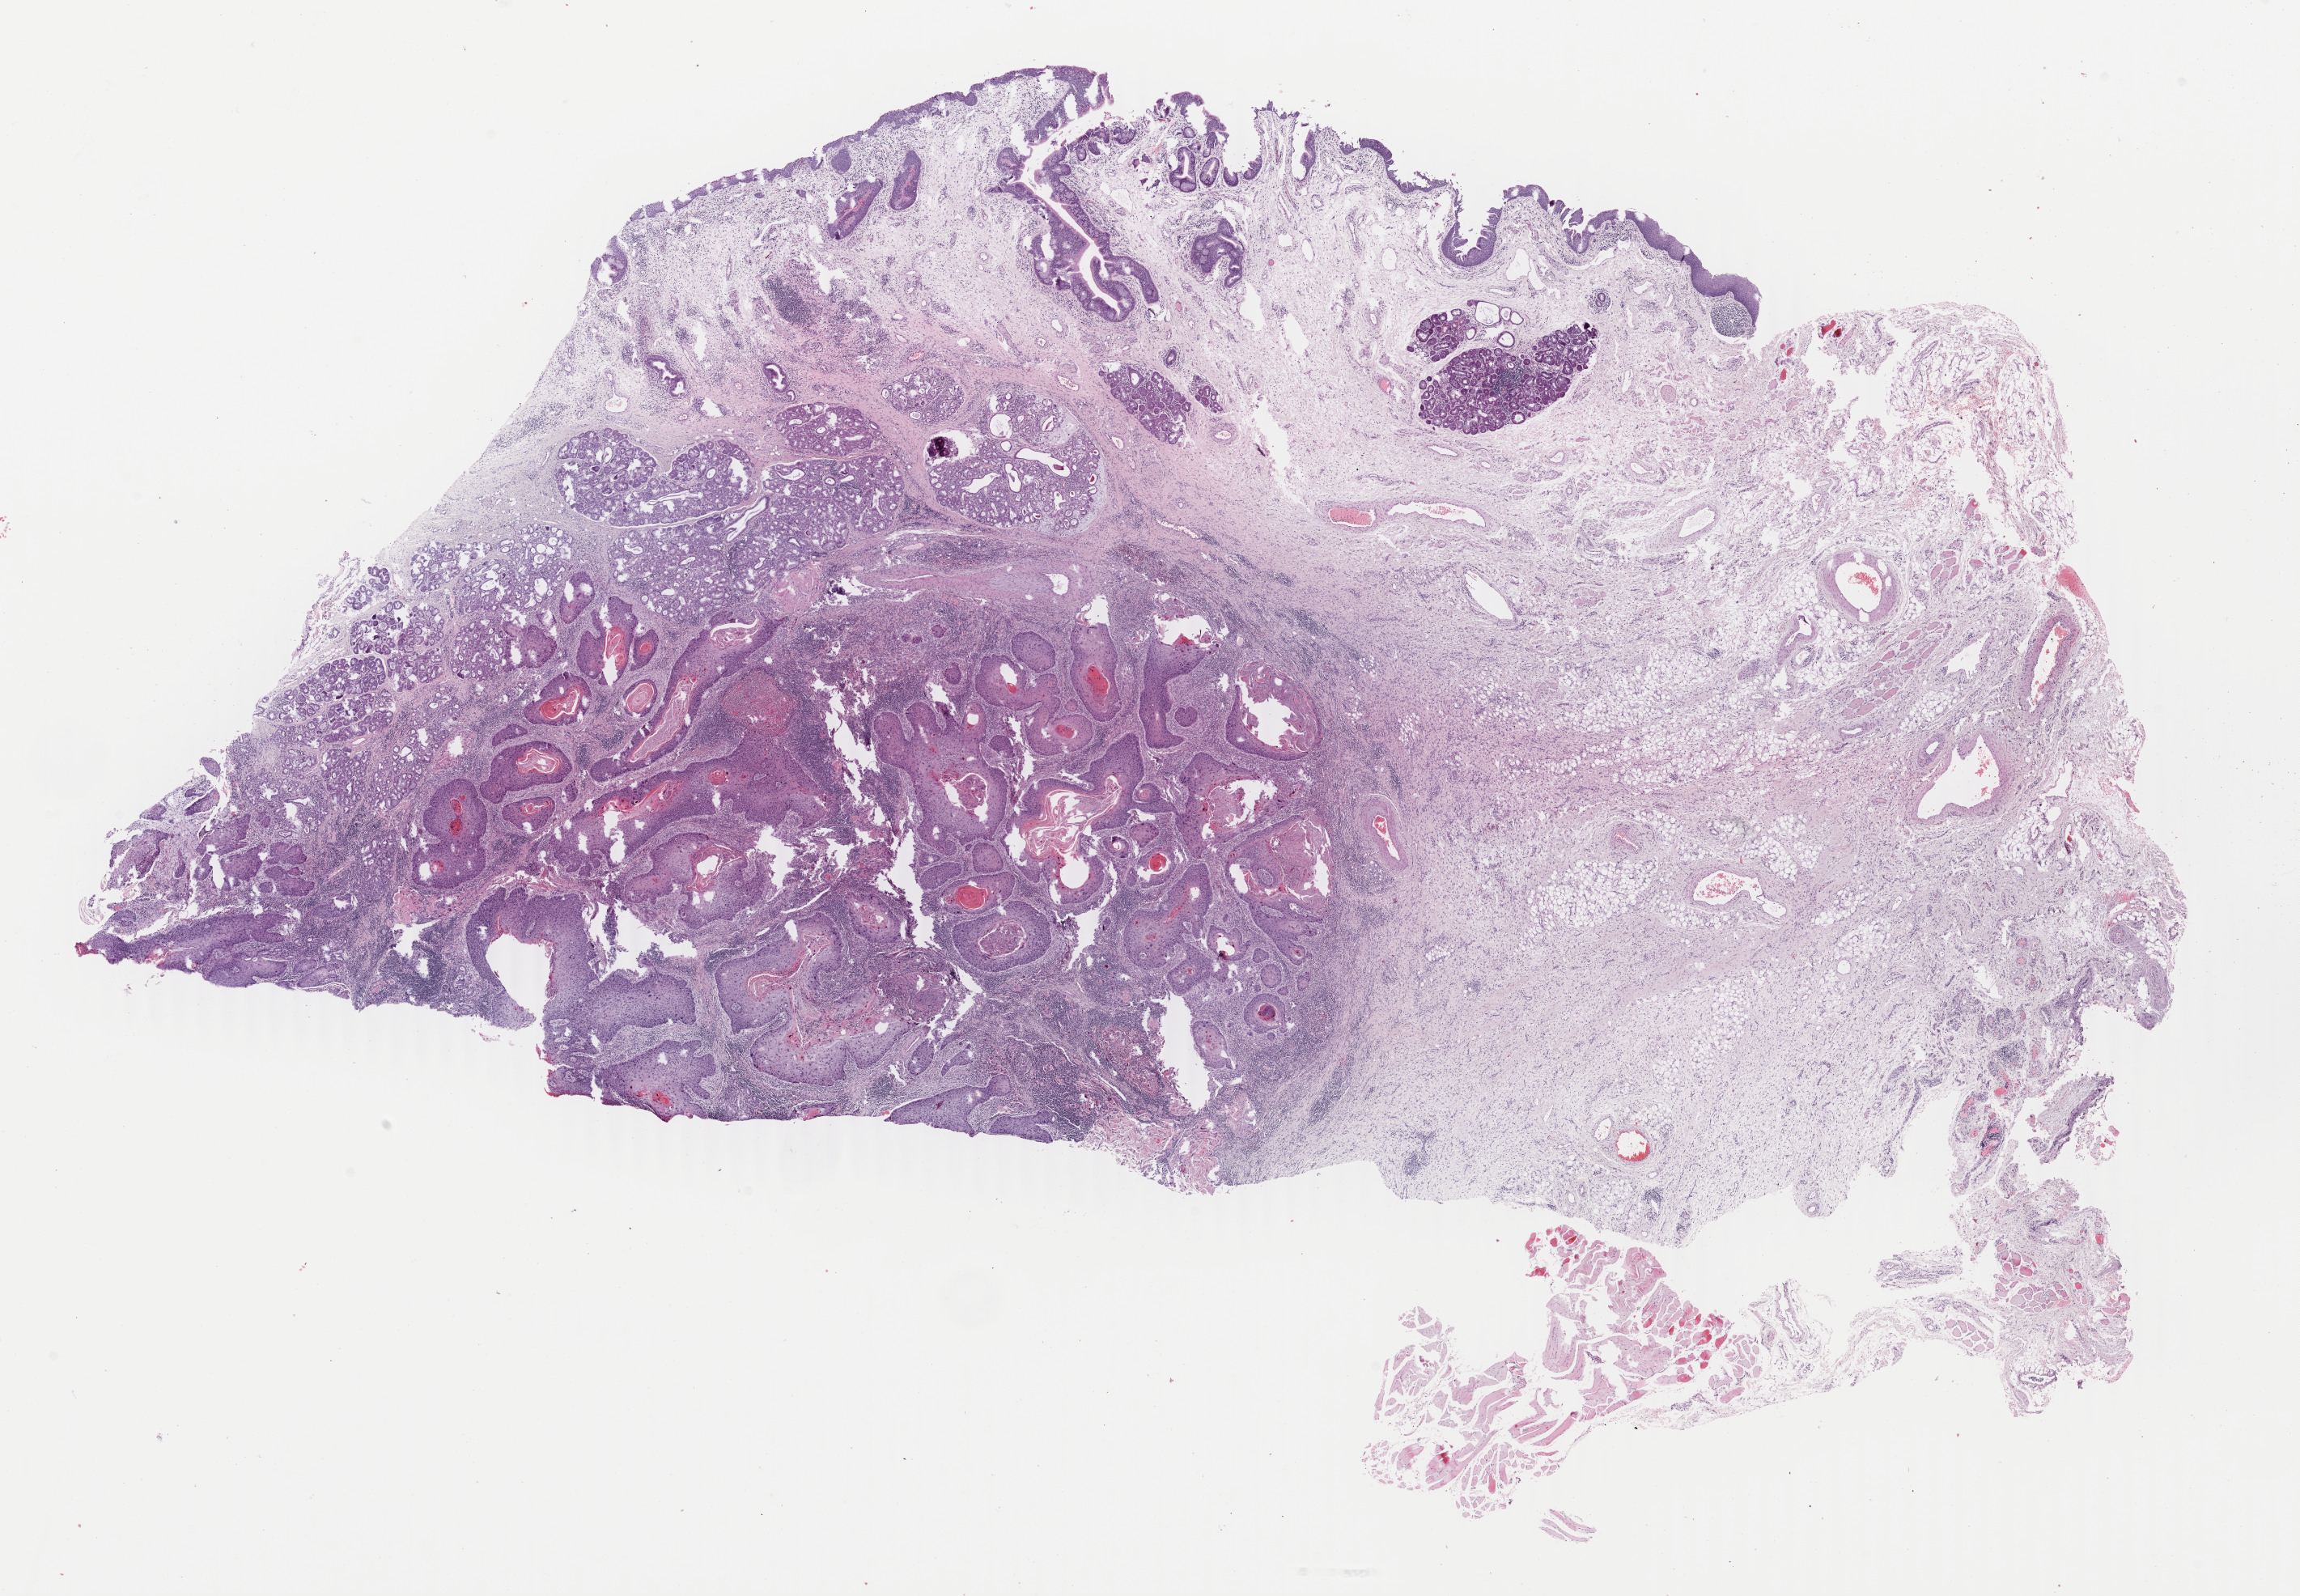
Digitized H&E tissue section (whole slide) — whole scanned area (about 22.6 x 15.7 mm) shown as a low-resolution overview; formalin-fixed paraffin-embedded (FFPE) diagnostic section; primary tumour sample from the head and neck. Male patient; age at initial diagnosis 61 years. Histologic grade: G2 (moderately differentiated).
* AJCC pathologic stage: III (7th edition)
* diagnosis: Squamous cell carcinoma, keratinizing, NOS (tongue, NOS)
* TNM: T3 N0 M0
* laterality: right